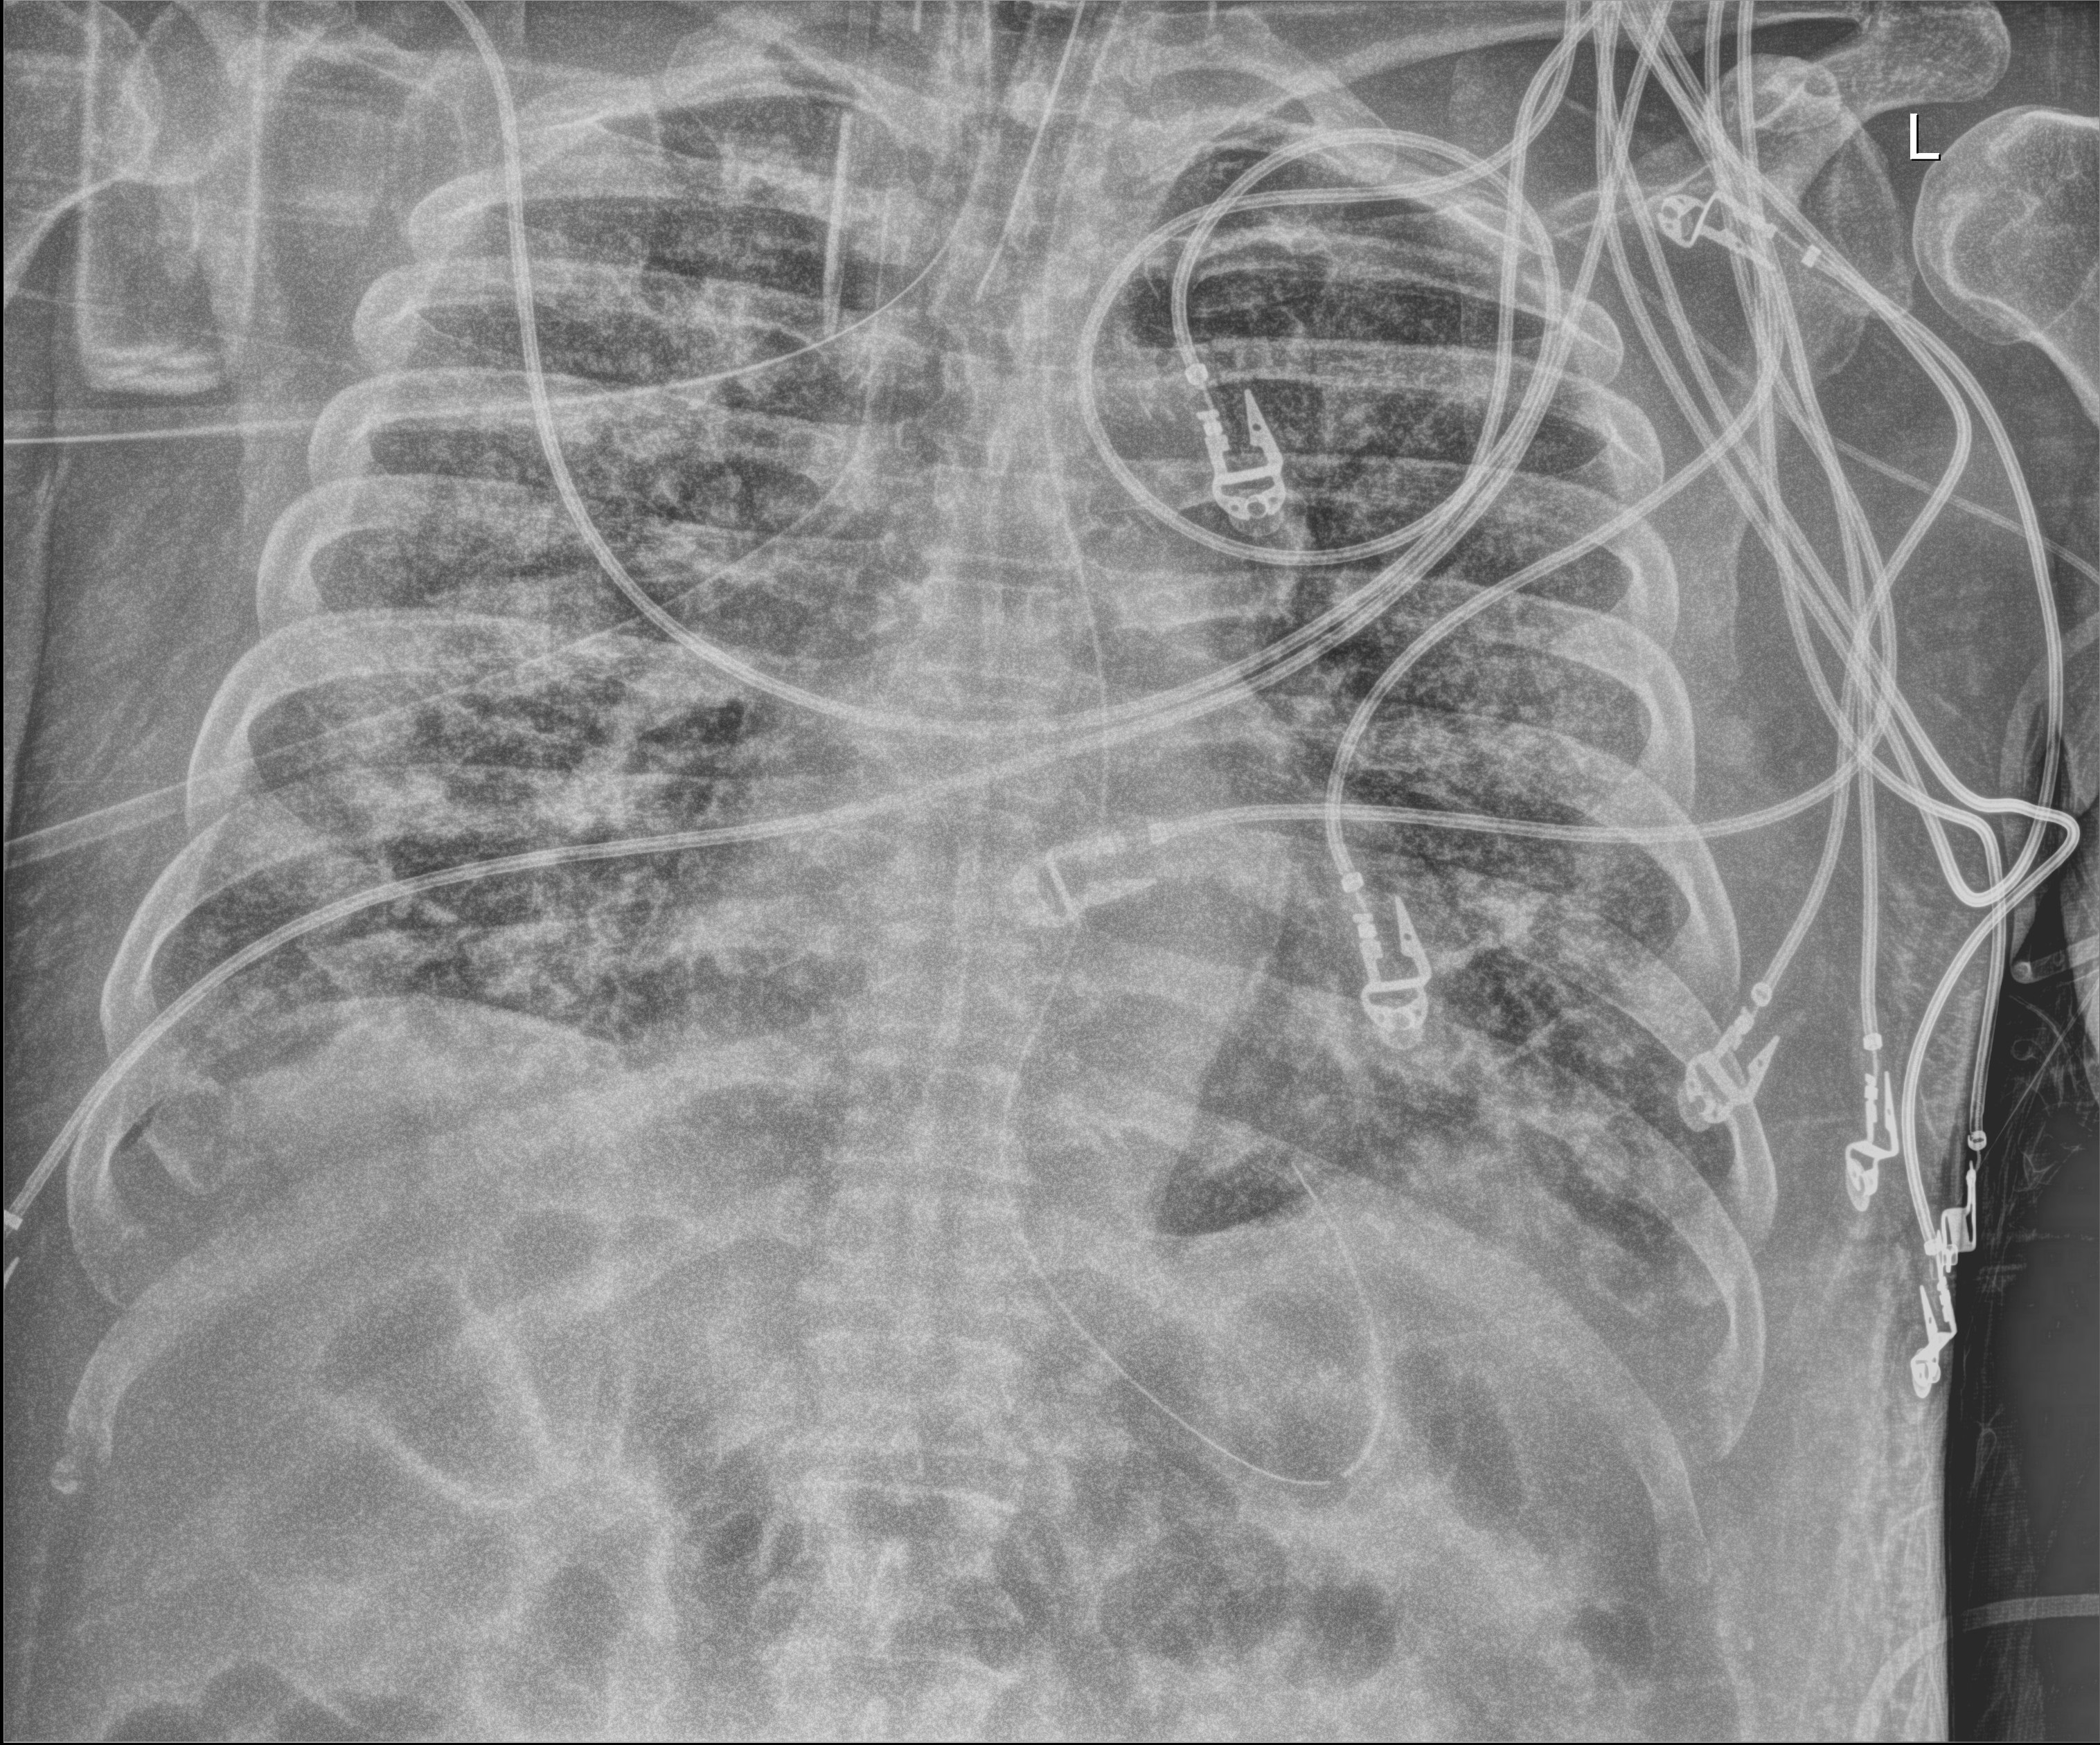
Bedside chest radiograph (digital radiography); anteroposterior (AP) projection. Patient hospitalised with COVID-19; male, aged 60–74 years.
Hospital-stay facts (about this admission, not read from this image; timing relative to this image not recorded):
- mechanically ventilated during this hospital stay: yes
- admitted to intensive care during this hospital stay: yes
- COPD (admission record): no